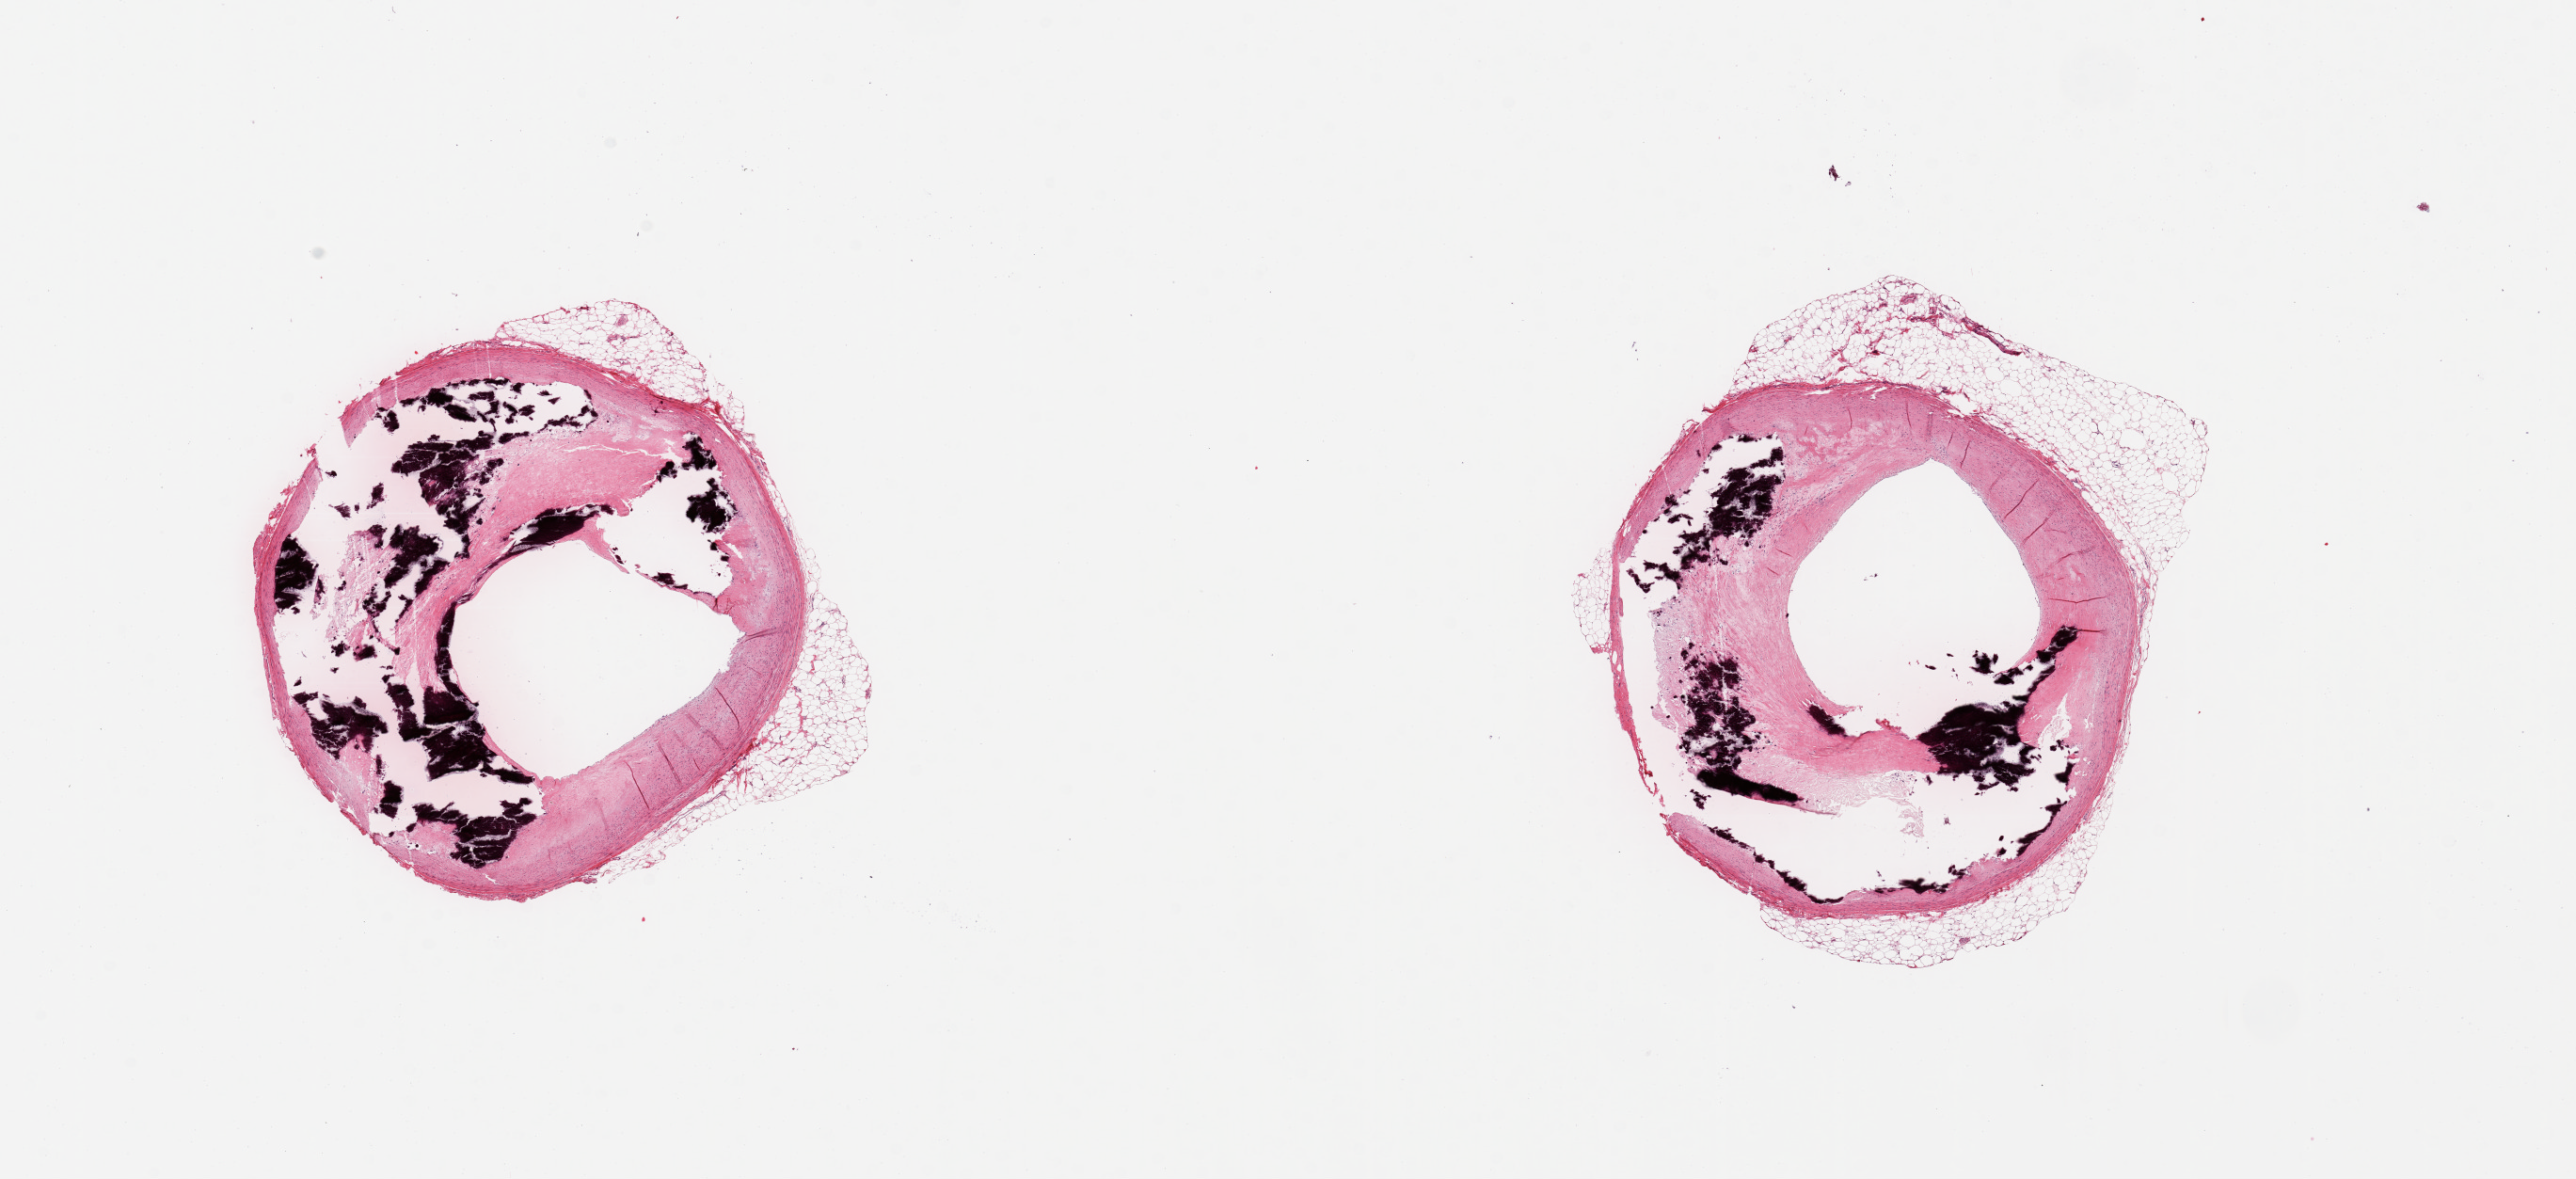
Whole-slide image, hematoxylin and eosin (H&E) stain — a low-resolution overview of the entire scanned area, about 21.7 x 9.9 mm, PAXgene-fixed paraffin-embedded (PFPE) section, section of coronary artery (target tissue), donor tissue sample. Donor sex: male.
- review note (as recorded): 2 pieces; severe calcific atherosclerosis with narrowing of the lumen, residual attached fat up to 1.1 mm